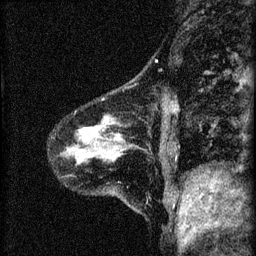
Breast MRI (dynamic contrast-enhanced), one sagittal slice; position 10 of 60 along the scan axis; dynamic contrast-enhanced series, image 2 of 4 at this slice position (ordered by acquisition); 1.5 T; TE 4.2 ms, TR 8.2 ms; 2 mm slice thickness; 256 × 256 image matrix, field of view 180 × 180 mm. Patient: female, 41 years.
Structures marked on this image (semi-automatic segmentation, software-assisted and operator-edited):
- analysis volume of interest (the breast-tissue region the enhancement analysis was run in; not a lesion): bounding box [x1, y1, x2, y2] px = [67, 103, 166, 192]
- tumour enhancement mask (voxels above the 70 % enhancement threshold inside the analysis volume of interest): [91, 131, 114, 156]